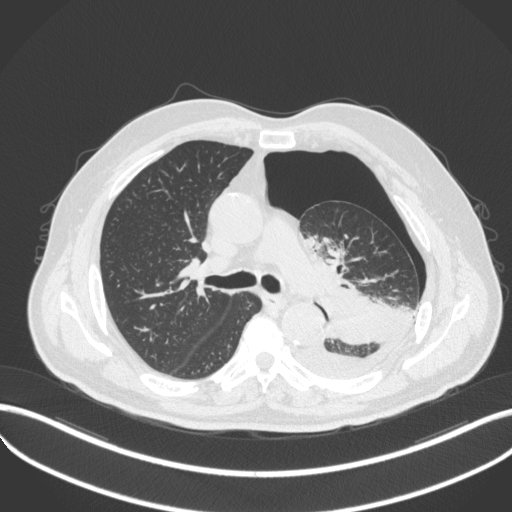
Chest CT, one axial slice. Reconstruction kernel B31f. 120 kVp. Lung window (W 1500 / L -600 HU). 512 × 512 image matrix, field of view 400 × 400 mm. Patient: male, 76 years. Case-level facts recorded for this patient, not image findings: clinical TNM (as recorded): T3 N0 M1b.
Structures marked on this image (rectangle marked by the reading radiologist):
- lung tumour (recorded histology: adenocarcinoma): bounding box [x1, y1, x2, y2] px = [315, 281, 396, 353]